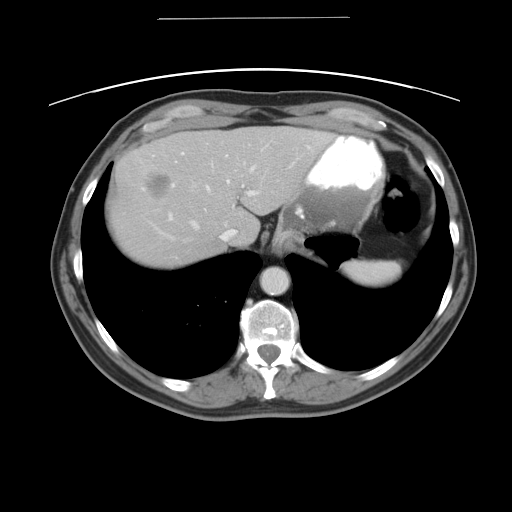
Contrast-enhanced abdominal CT, one axial slice; slice 38 of 49 in the series (ordered by position); 120 kVp; intravenous contrast given; soft-tissue window (W 400 / L 40 HU); 5 mm slice thickness; 512 × 512 image matrix. Male patient, age 57 years. From the clinical record (not read from this slice): diagnosis: colorectal cancer liver metastases, imaged before liver resection; multiple liver metastases: yes; largest metastasis: 4 cm; chemotherapy before resection: no.
Annotated regions visible in this slice (expert manual segmentation):
- hepatic veins: box from (x=151, y=165) to (x=253, y=238) px
- liver: (x=108, y=125)–(x=334, y=267)
- planned liver remnant (the part of the liver to remain after resection): (x=206, y=126)–(x=334, y=245)
- portal vein (with intrahepatic branches): (x=167, y=142)–(x=267, y=220)
- liver metastasis: (x=141, y=171)–(x=174, y=202)